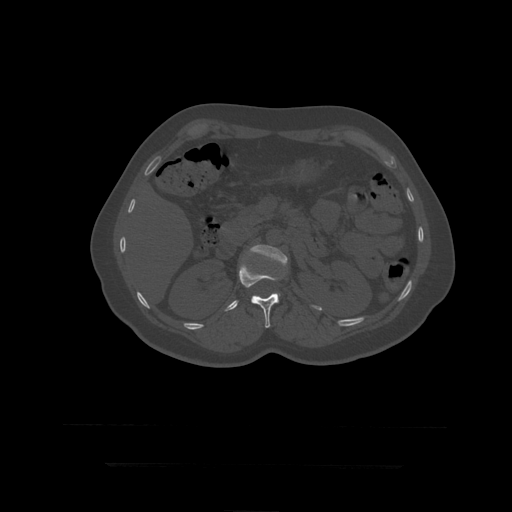
CT including the spine, one axial slice; position 167 of 399 along the scan axis; reconstruction kernel STANDARD; 120 kVp; bone window (W 1800 / L 400 HU); 1.25 mm slice thickness; 512 × 512 image matrix, field of view 450 × 450 mm. Patient age 41 years. Case-level facts recorded for this patient, not image findings: primary cancer: breast.
Structures marked on this image (semi-automatic segmentation, software-assisted and operator-edited):
- L1 vertebra: bounding box [x1, y1, x2, y2] px = [239, 264, 279, 328]
- L2 vertebra: [250, 245, 288, 296]